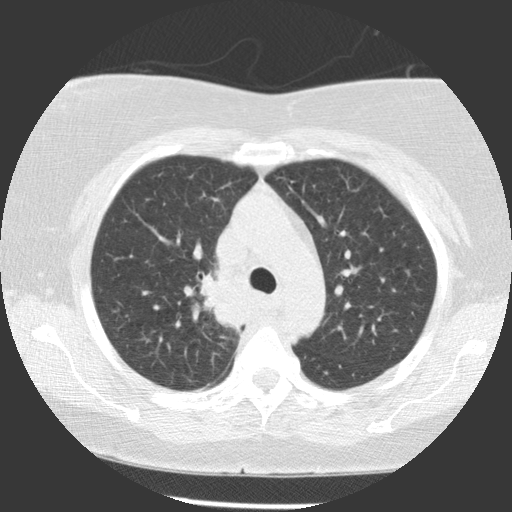
Chest CT (low-dose screening protocol), one axial image, baseline annual screen, lung window (W 1500 / L -600 HU), standard (soft-tissue) reconstruction kernel (STANDARD). Female, age 63 years at enrolment.
Expert-annotated lung lesion, bounding box [x1, y1, x2, y2] px = [190, 263, 251, 324]. The exam's reader record, not a measurement of the box and not confirmed to be the same lesion: non-calcified nodule or mass ≥4 mm, right upper lobe, 39 × 36 mm, spiculated (stellate) margins, soft tissue attenuation. Participant outcome: lung cancer diagnosed 72 days after this screen — non-small cell carcinoma, right upper lobe, carina, right main stem bronchus, poorly differentiated (G3), stage IIIA (AJCC 6th edition), 66 mm at pathology.